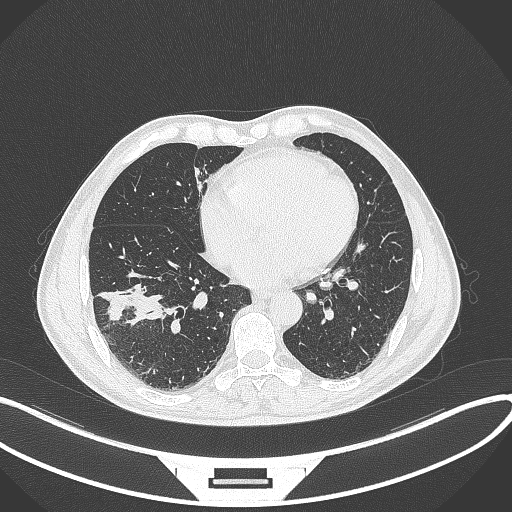
Chest CT, one axial slice; position 136 of 364 along the scan axis; reconstruction kernel B70f; 120 kVp; lung window (W 1500 / L -600 HU); 1 mm slice thickness; 512 × 512 image matrix. Patient: male, 58 years. From the clinical record (not read from this slice): clinical TNM (as recorded): T3 N0 M0; histopathological grade: G2.
Outlined on this slice (rectangle marked by the reading radiologist):
- lung tumour (recorded histology: squamous cell carcinoma): bounding box (x1, y1, x2, y2) in pixels: (103, 284, 165, 325)